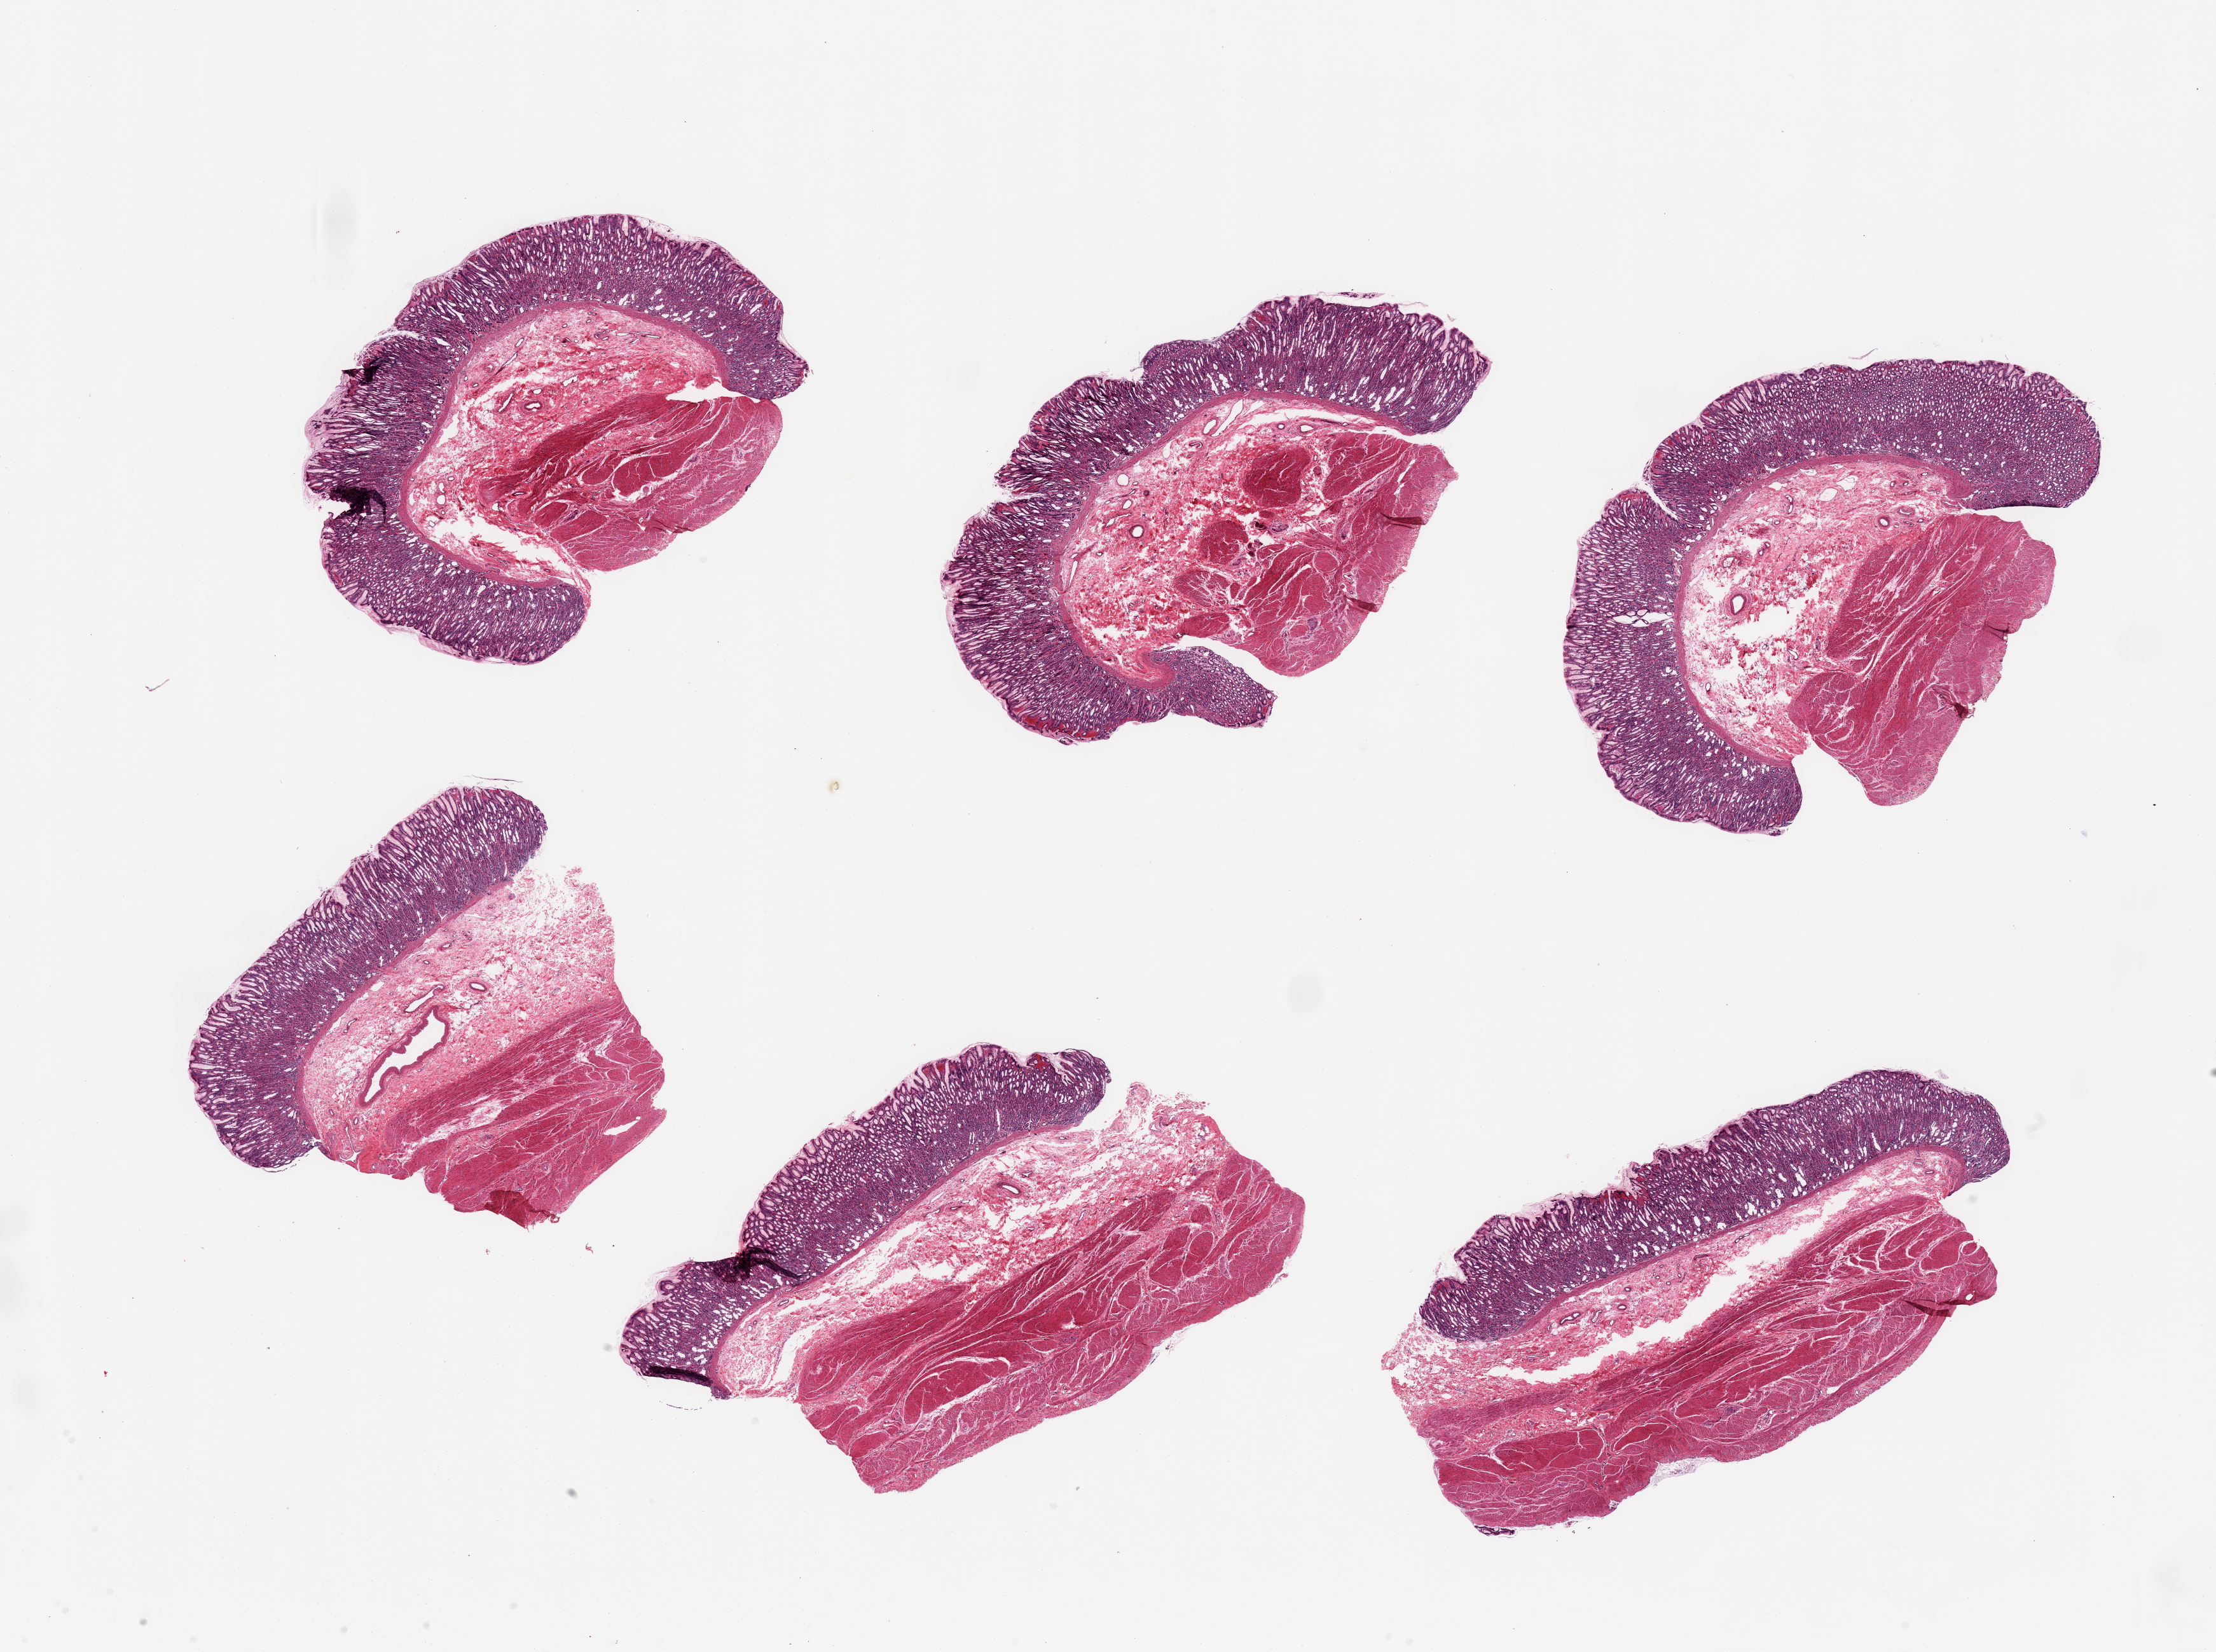
Digitized haematoxylin and eosin-stained section — whole scanned area (about 27.6 x 20.5 mm) shown as a low-resolution overview; PAXgene-fixed paraffin-embedded (PFPE) section; sampled site (target tissue): stomach; donor tissue sample. Donor: male.
• pathologist's review note for this sample: 6 pieces; full thickness gastric wall; preserved gastric mucosa and muscularis; mild to moderate autolysis of submucosa